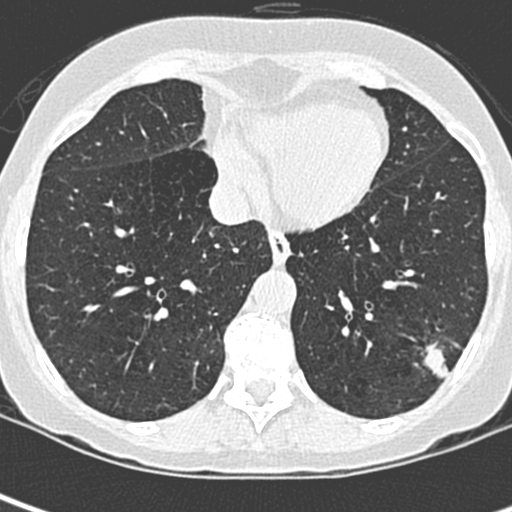
Low-dose screening chest CT, one axial slice. Slice 92 of 252 in the series (ordered by position). 120 kVp. Lung window (W 1500 / L -600 HU). 512 × 512 image matrix, field of view 271 × 271 mm.
Annotated regions visible in this slice (expert manual segmentation):
- lesion 1 (tumor, lower lobe of left lung): box from (x=423, y=347) to (x=449, y=379) px